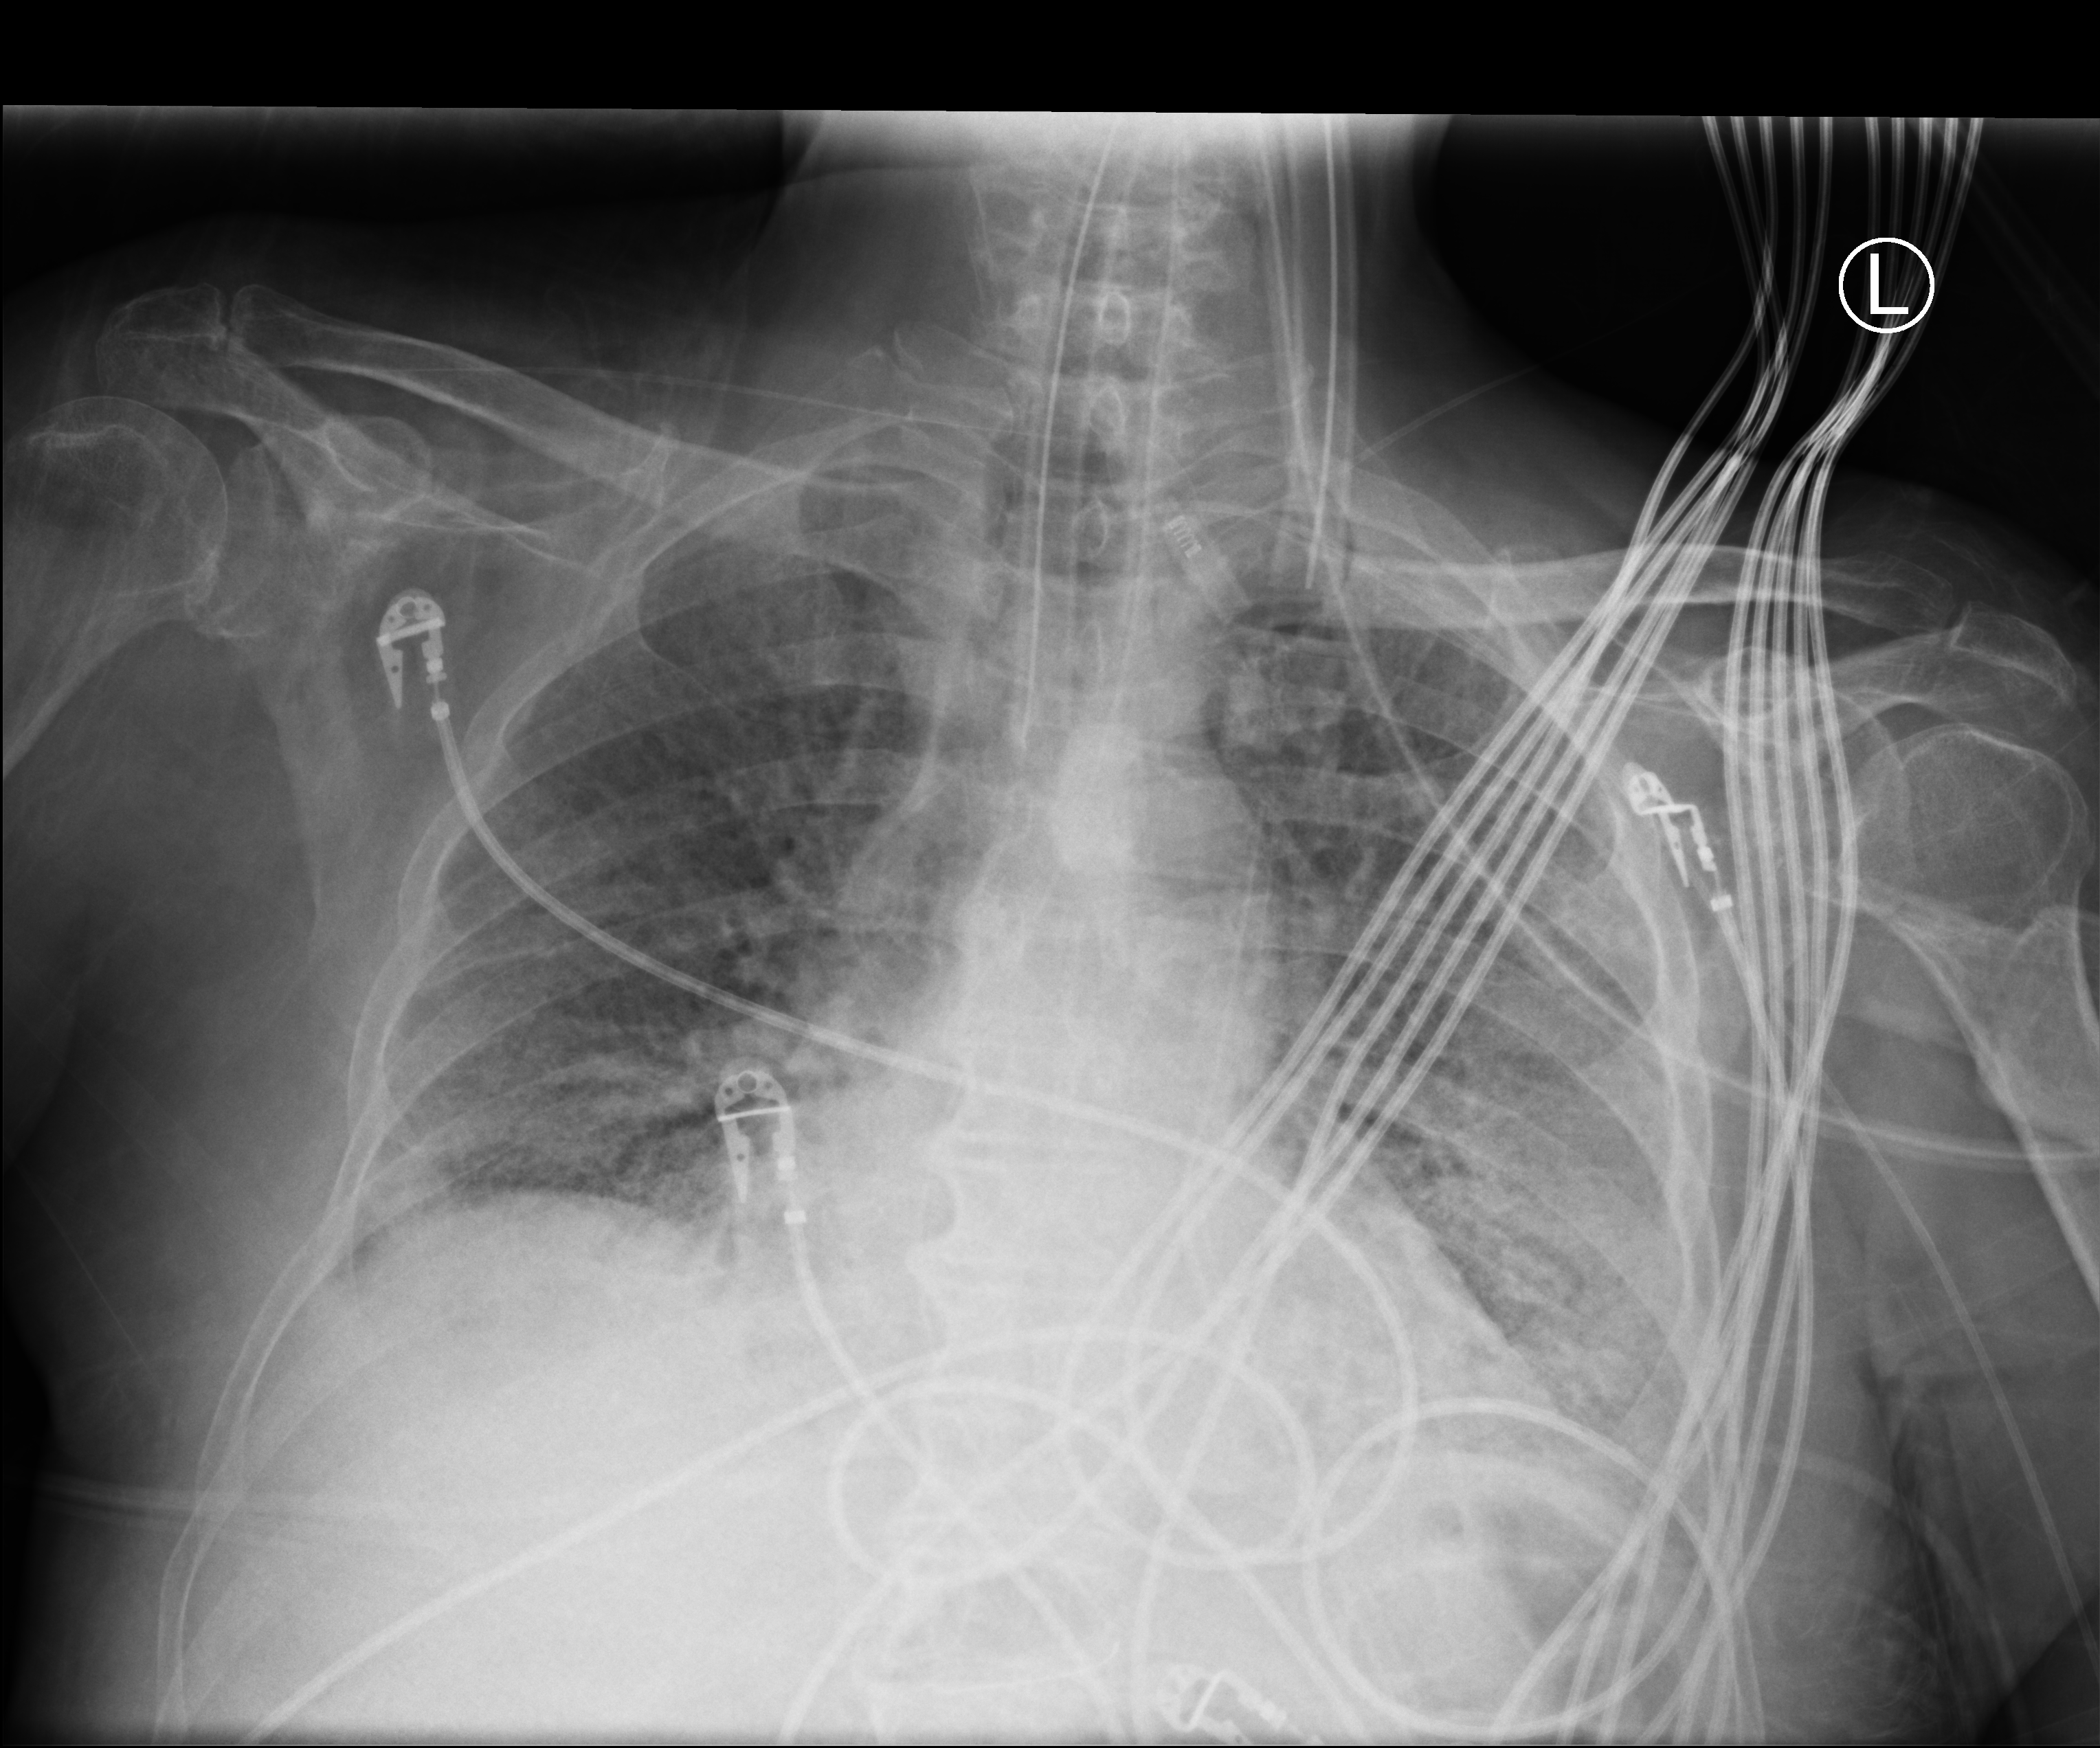
Chest X-ray (portable), anteroposterior (AP) projection. Patient hospitalised with COVID-19; male, aged 75–90 years.
Hospital-stay facts (about this admission, not read from this image; timing relative to this image not recorded): admitted to intensive care during this hospital stay: yes.